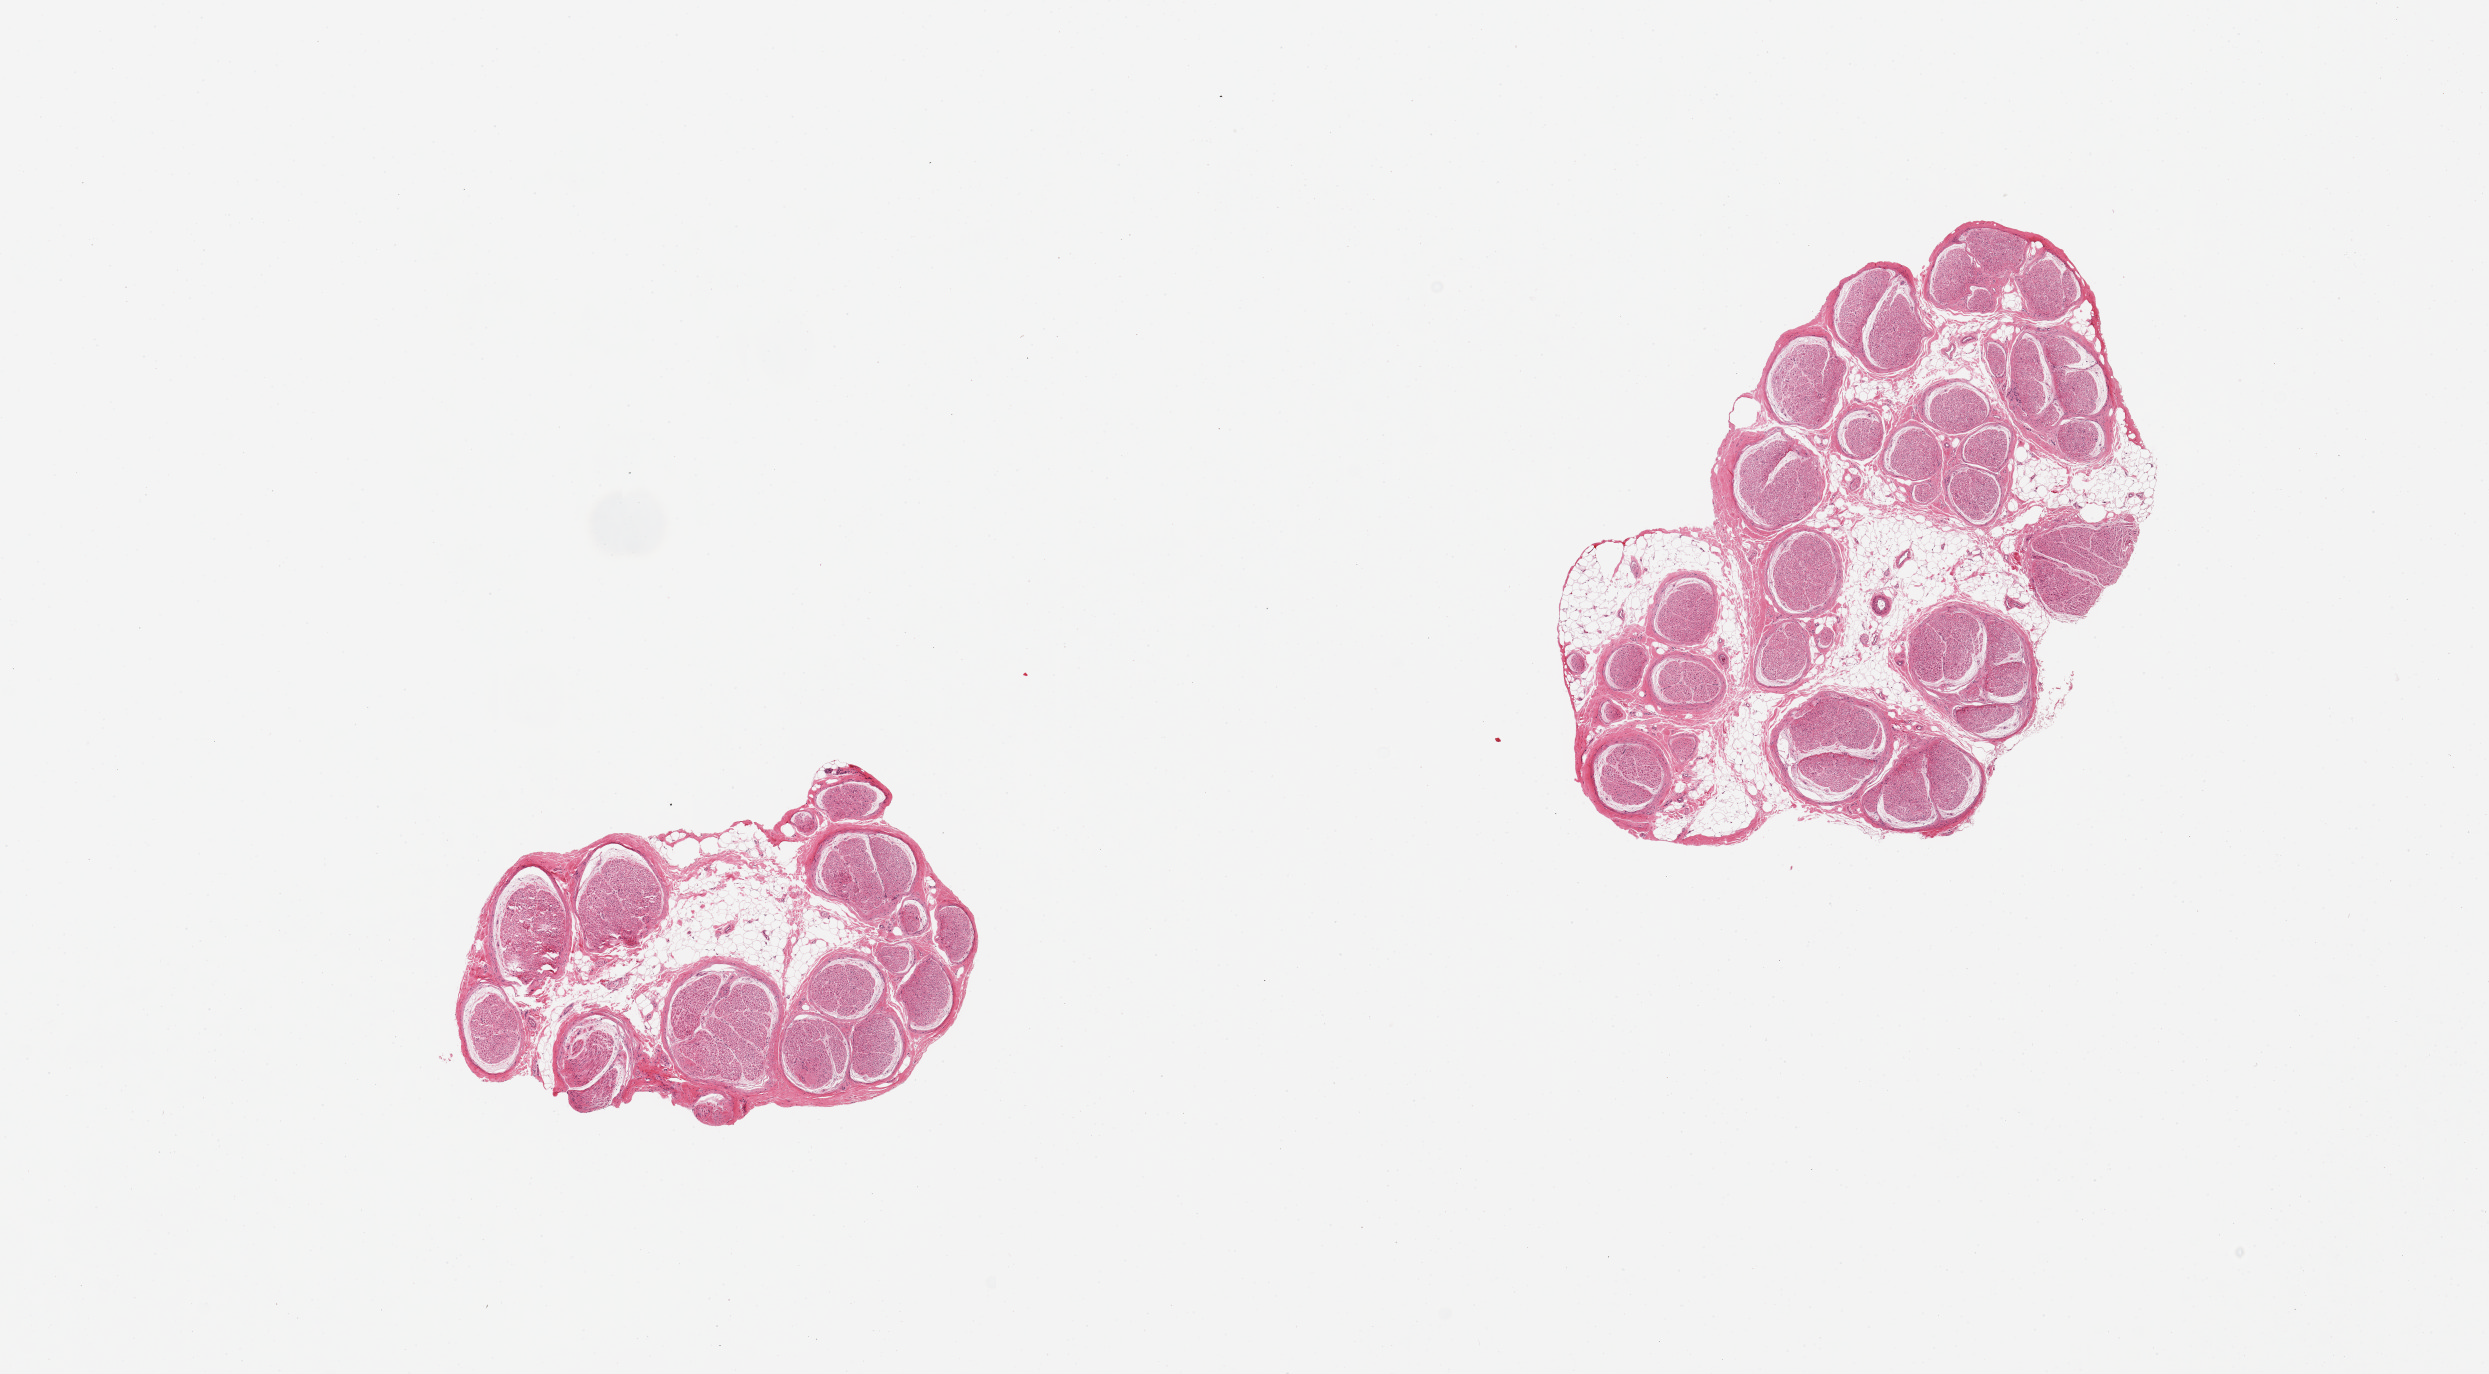
Whole-slide image, hematoxylin and eosin (H&E) stain, a low-resolution overview of the entire scanned area, about 19.7 x 10.9 mm. PAXgene-fixed, paraffin-embedded tissue. Section of tibial nerve (target tissue). Donor tissue sample.
- reviewer comment on this tissue sample: 2 pieces. 20% internal fat